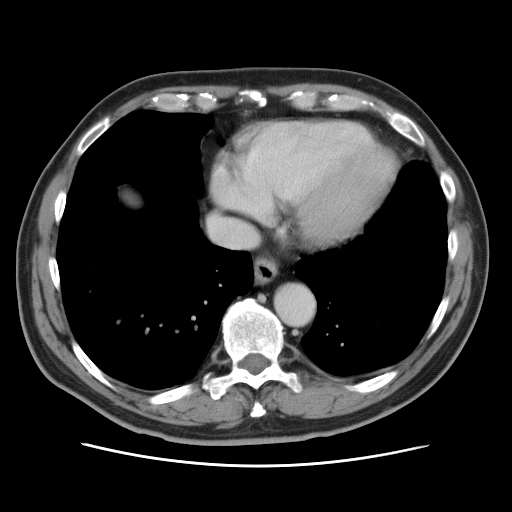
Contrast-enhanced abdominal CT, one axial slice. Position 76 of 80 along the scan axis. 120 kVp. Intravenous contrast given. Soft-tissue window (W 400 / L 40 HU). 5 mm slice thickness. 512 × 512 image matrix, field of view 370 × 370 mm. Male patient, age 69 years. Case-level facts recorded for this patient, not image findings: diagnosis: colorectal cancer liver metastases, imaged before liver resection; multiple liver metastases: no; largest metastasis: 5 cm; disease in both lobes: yes.
Annotated regions visible in this slice (manually delineated by an expert):
- hepatic veins: bounding box [x1, y1, x2, y2] px = [209, 216, 252, 247]